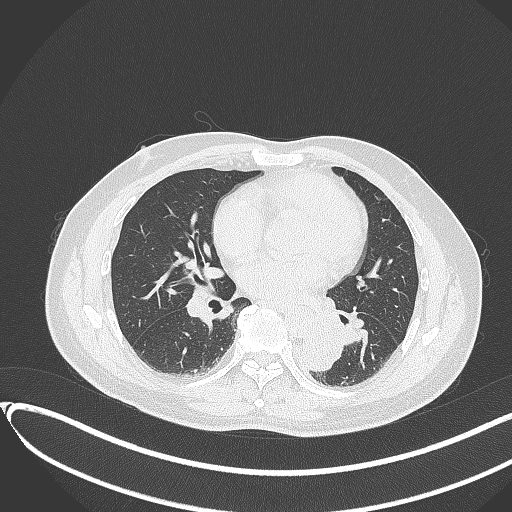
Chest CT, one axial slice; position 155 of 417 along the scan axis; lung window (W 1500 / L -600 HU); 512 × 512 image matrix, field of view 400 × 400 mm. Male patient, age 54 years. From the clinical record (not read from this slice): clinical TNM (as recorded): T3 N0 M0.
Structures marked on this image (bounding box drawn by a radiologist):
- lung tumour (recorded histology: squamous cell carcinoma): bounding box [x1, y1, x2, y2] px = [294, 329, 348, 377]